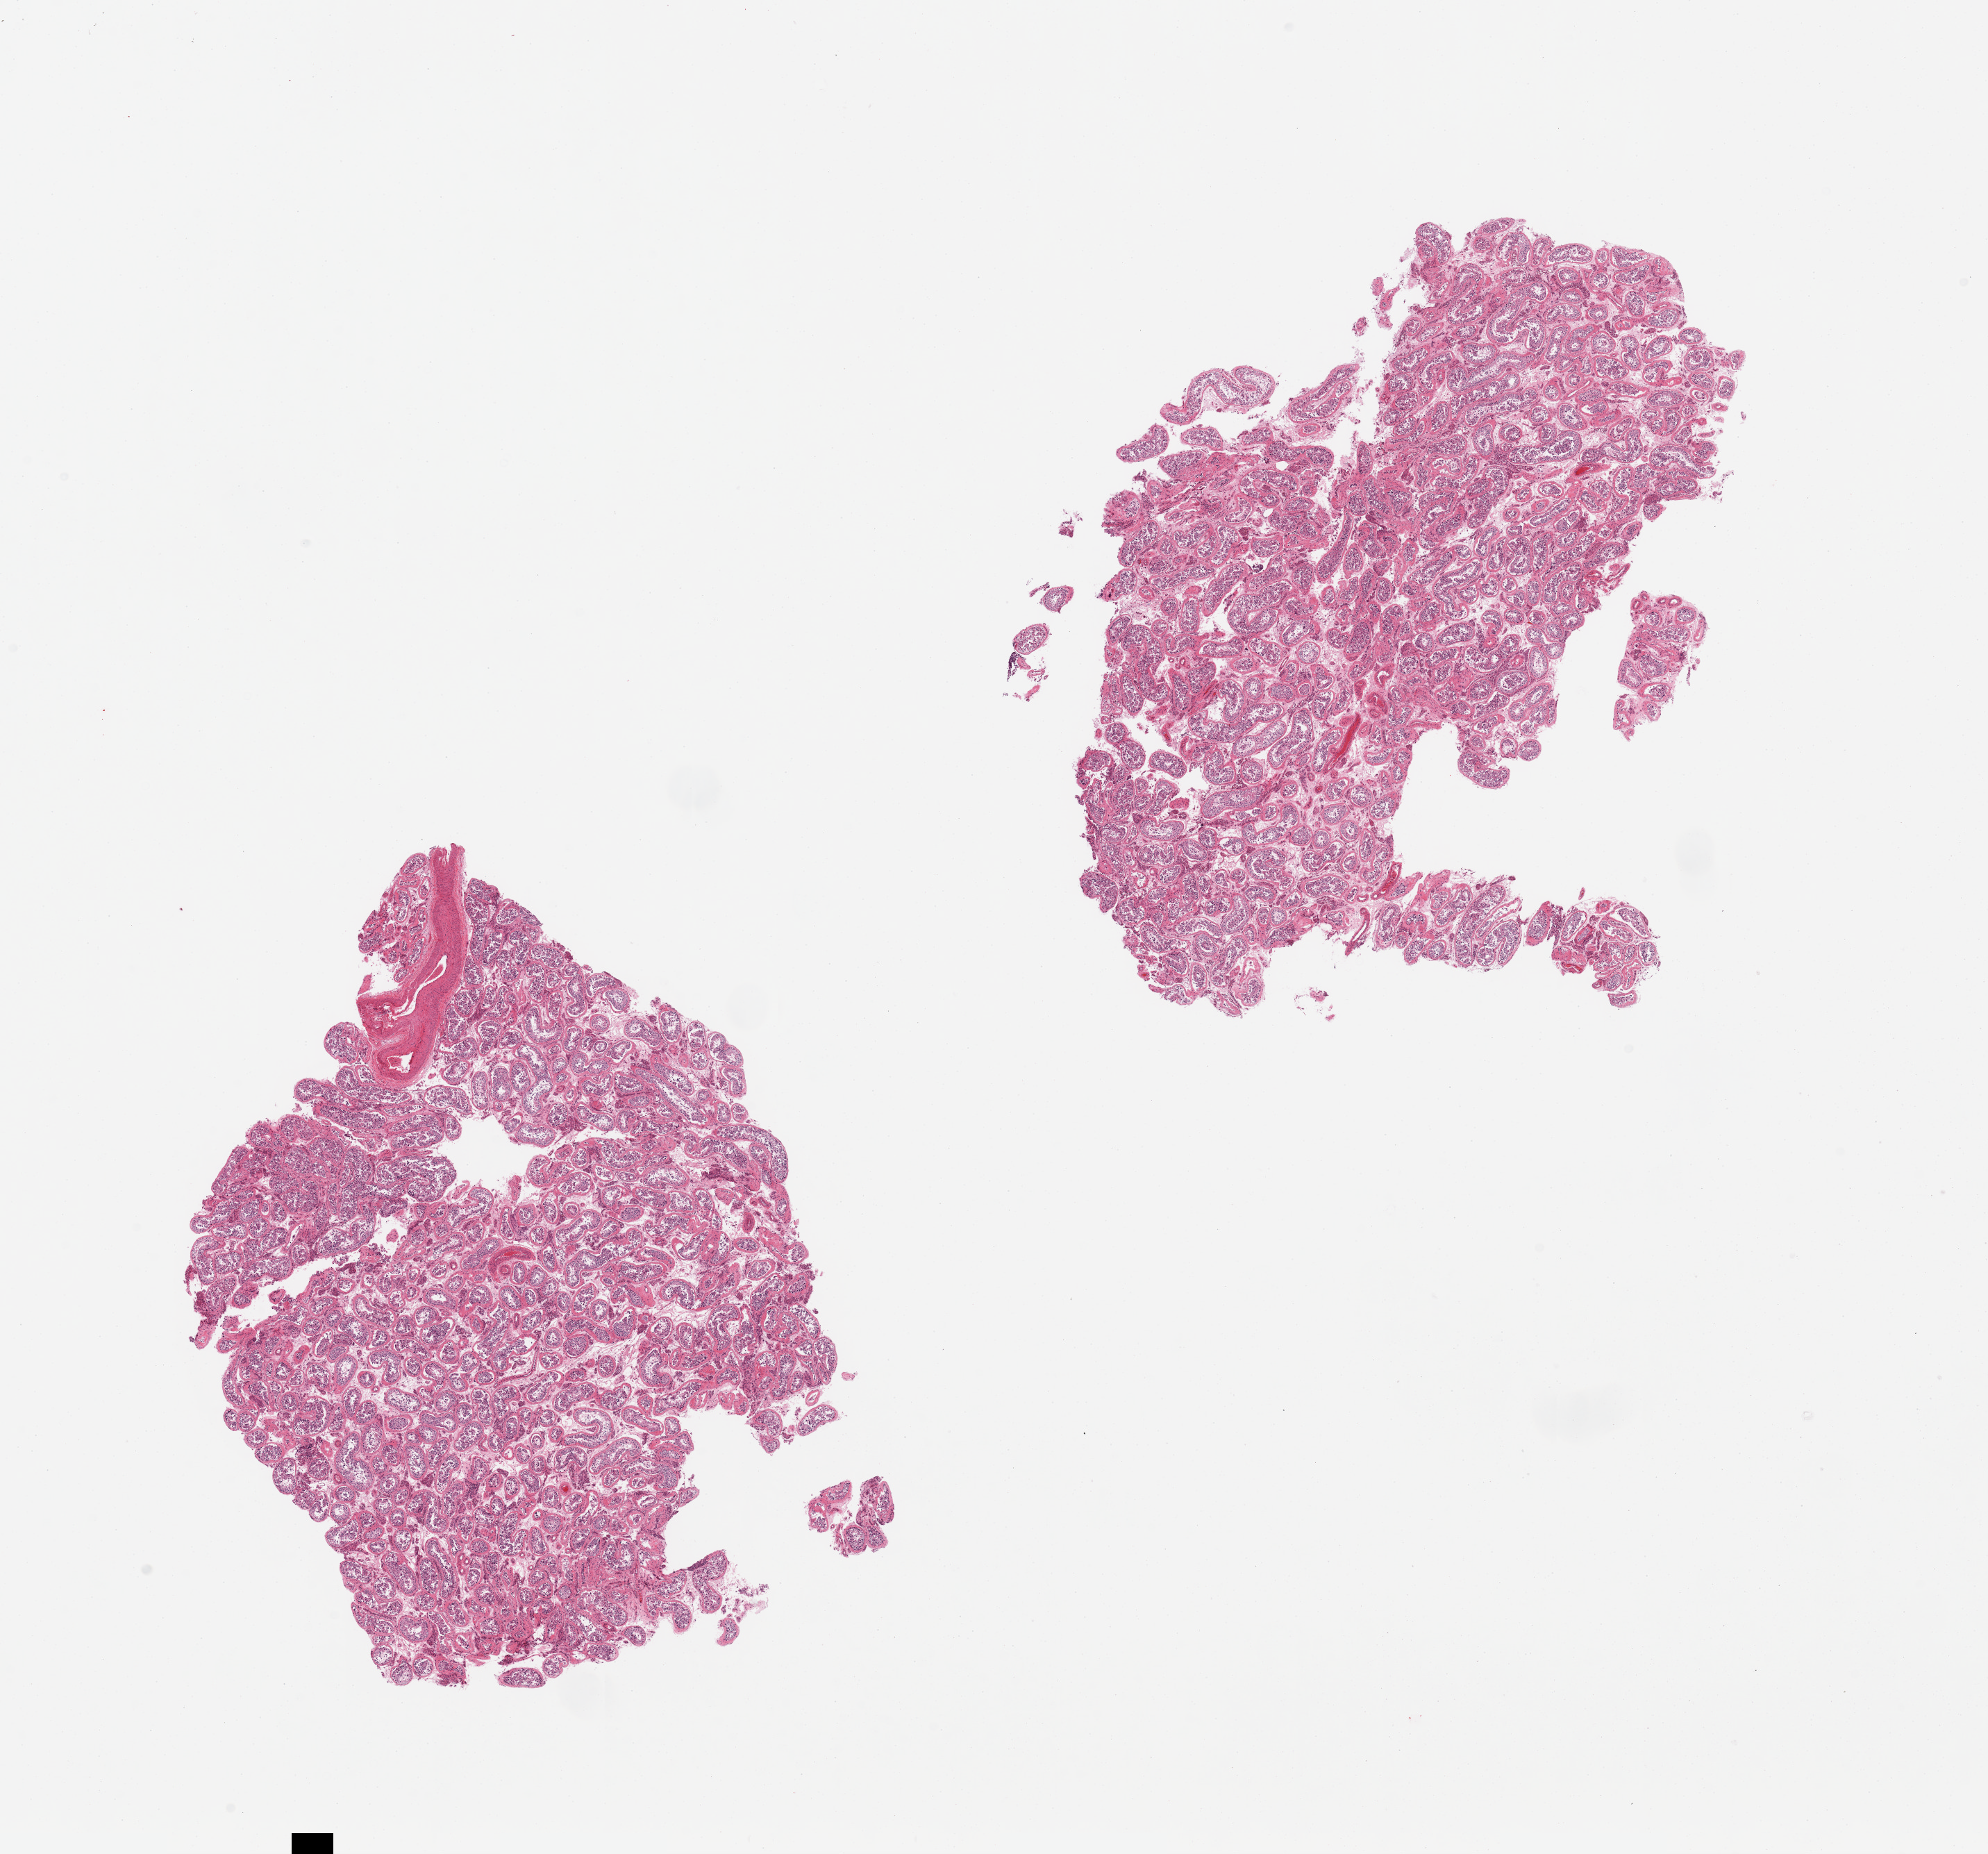
Haematoxylin and eosin whole-slide image, shown as a low-resolution overview of the whole scanned area (about 22.6 x 21.1 mm, from a 20x scan); PAXgene-fixed, paraffin-embedded tissue; sampled site (target tissue): testis; donor tissue sample. Donor: male.
Review note (as recorded): 2 pieces, autolysis variable from mild--moderate/severe. Spermatogenesis present, but appears reduced.